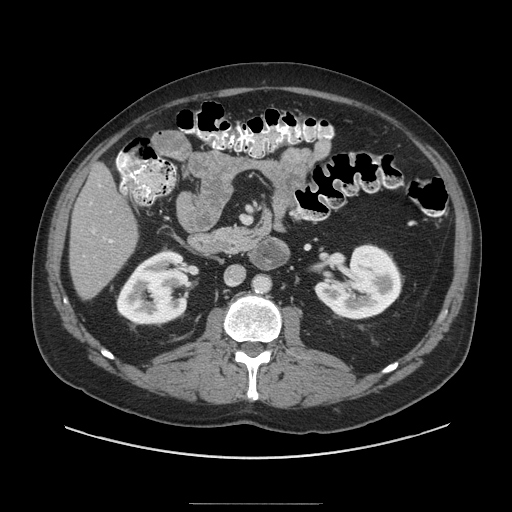
Contrast-enhanced abdominal CT (liver protocol), one axial slice; position 32 of 91 along the scan axis; soft-tissue window (W 400 / L 40 HU); 2.5 mm slice thickness; 512 × 512 image matrix, field of view 440 × 440 mm. Case-level facts recorded for this patient, not image findings: diagnosis: hepatocellular carcinoma (patient treated with transarterial chemoembolisation; whether this scan precedes or follows treatment is not stated here); TNM stage (as recorded): Stage-I; Child-Pugh class: A; tumour differentiation: well differentiated; tumour nodularity: uninodular.
Annotated regions visible in this slice (semi-automatically segmented with operator editing):
- liver parenchyma outside the tumour (the mass and vessels are separate outlines, so this box may not span the whole liver): bounding box [x1, y1, x2, y2] px = [70, 164, 138, 297]
- liver vessels: [92, 230, 114, 243]